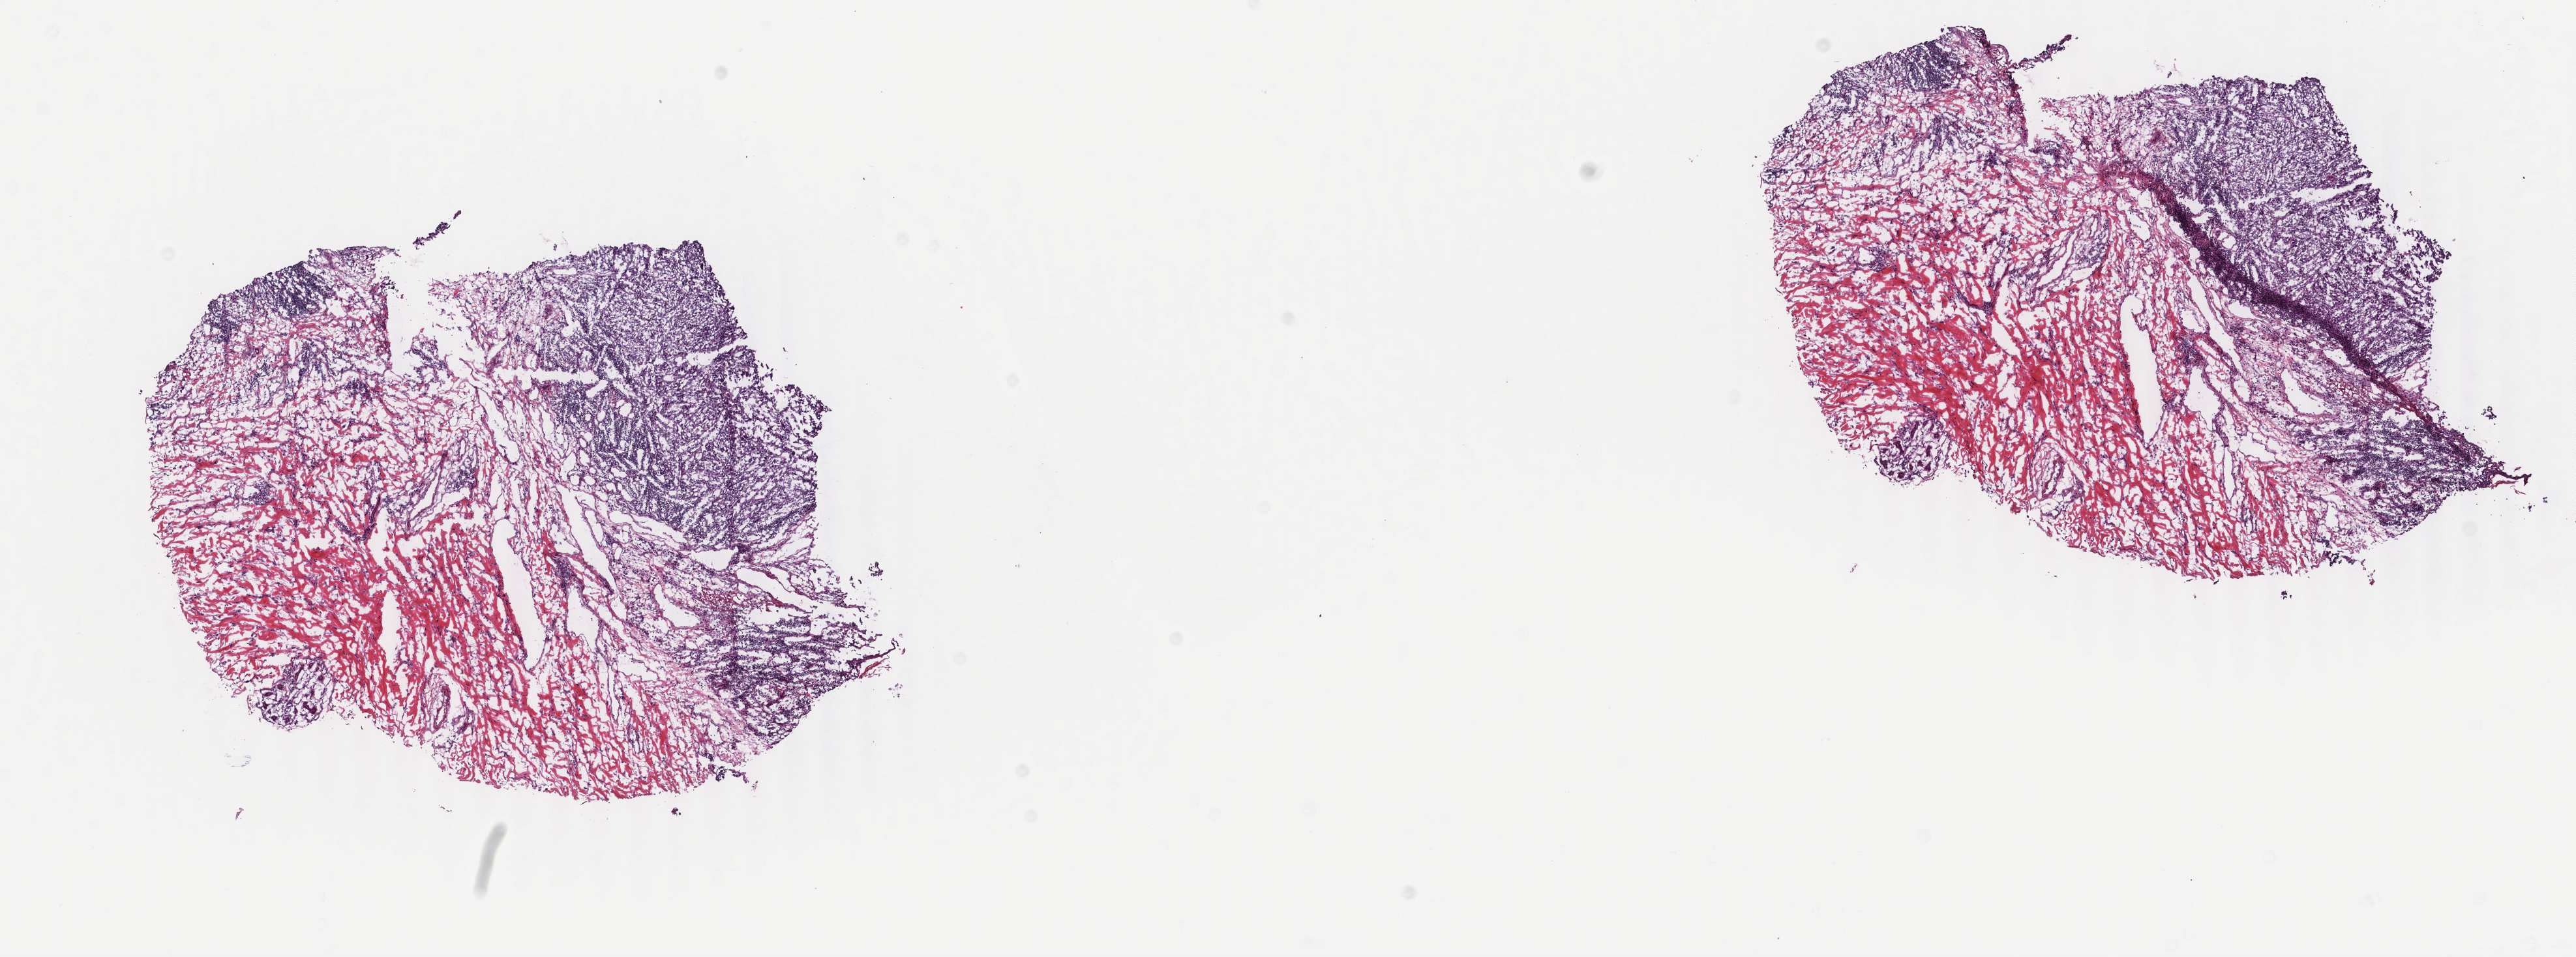
Whole-slide histology image, H&E, whole scanned area (about 15.7 x 5.8 mm, from a 40x scan) shown as a low-resolution overview; frozen section; skin, primary tumour sample. Male, age 80 years at initial diagnosis. Composition of this section per pathologist review: tumour cells 45%, tumour nuclei 70%, normal cells 0%, stromal cells 55%, necrosis 0%. Inflammatory infiltration, as recorded: lymphocyte infiltration 0%, monocyte infiltration 0%, neutrophil infiltration 0%.
Diagnosis: Malignant melanoma, NOS. AJCC pathologic stage: IIC (7th edition).